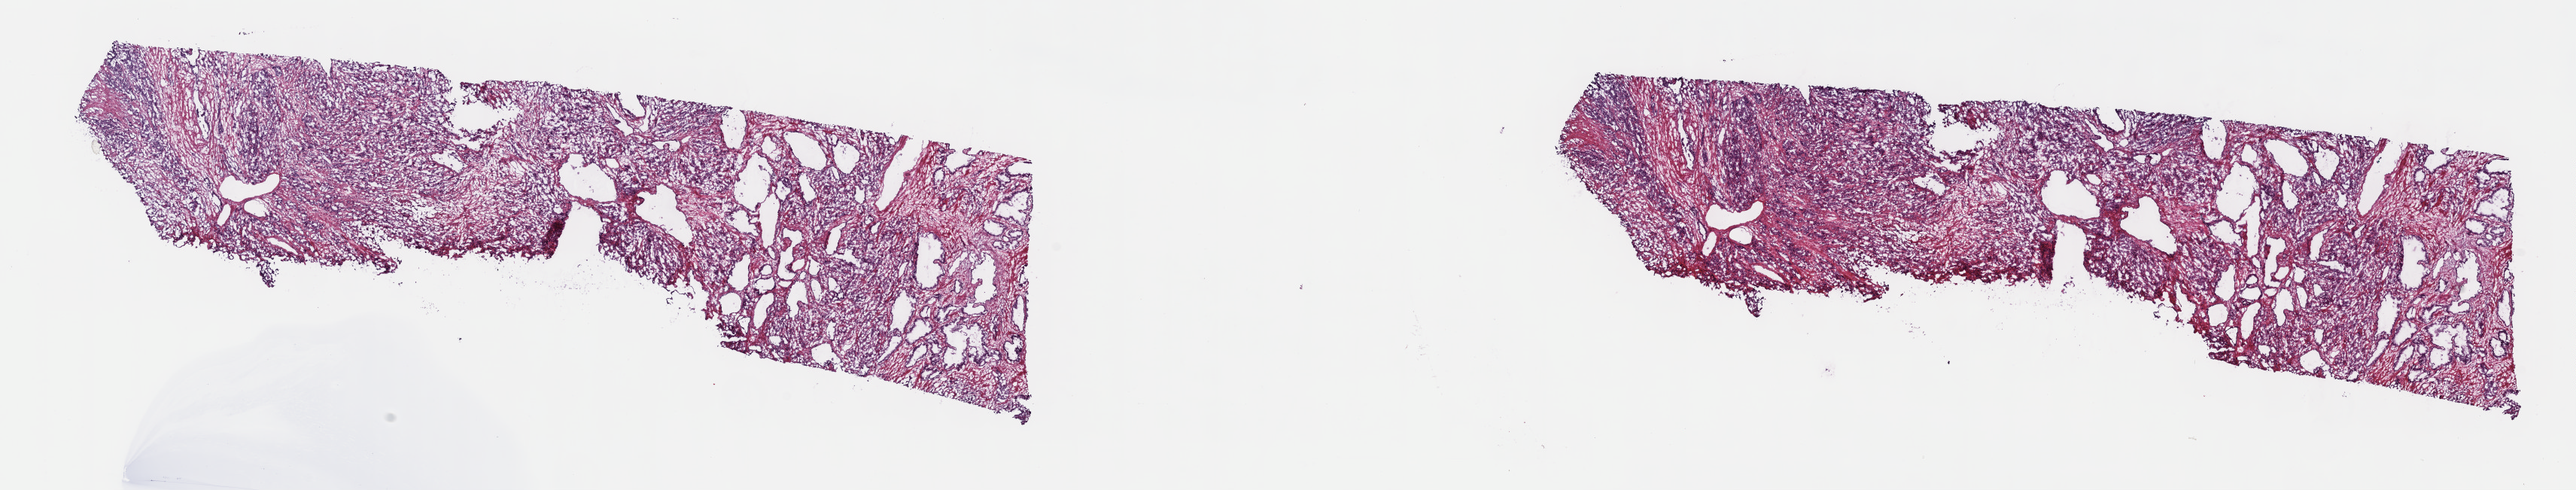
Whole-slide histology image, Hematoxylin and eosin (H&E) stained — whole scanned area (about 27.7 x 5.3 mm, from a 40x scan) shown as a low-resolution overview; frozen section; prostate, primary tumour sample. Patient: male, age at initial diagnosis 67 years. Gleason score: 9 (5+4). Pathologist review of this section (percent, as recorded): tumour cells 100%, tumour nuclei 70%, normal cells 0%, stromal cells 0%, necrosis 0%. Infiltration values recorded for this section: lymphocyte infiltration 1%, monocyte infiltration 0%, neutrophil infiltration 0%.
Laterality: bilateral. Lymph nodes positive (case pathology): 0 of 7 examined. Diagnosis: Adenocarcinoma, NOS (prostate gland).